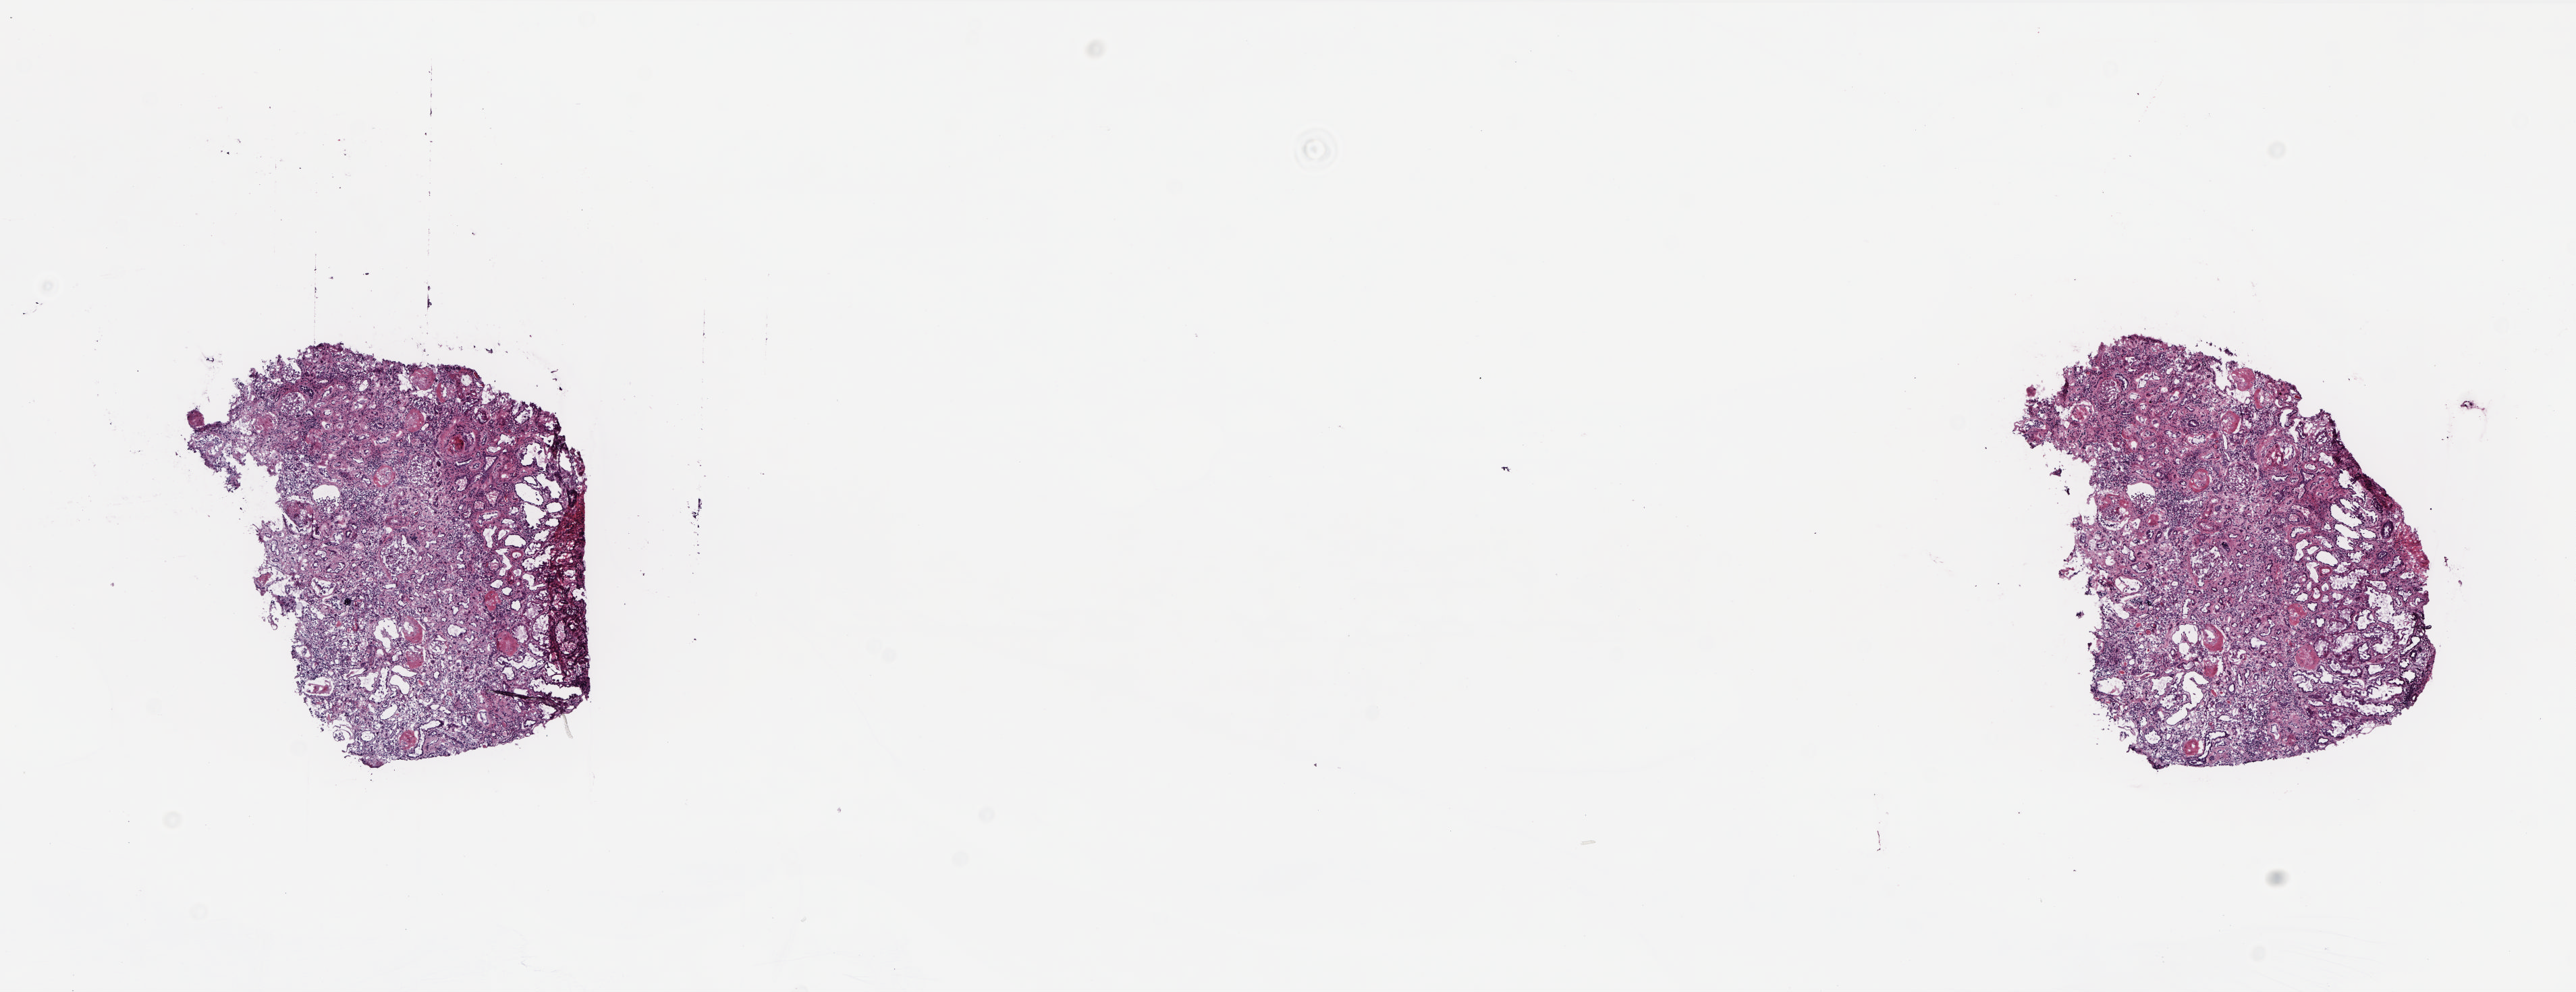
Whole-slide histology image, H&E, a low-resolution overview of the entire scanned area, about 15.4 x 5.9 mm, frozen section from the top of the tissue portion, kidney, solid tissue normal (non-tumour tissue) sample. Male, age 46 years at initial diagnosis. Pathologist review of this section (percent, as recorded): tumour cells 0%, tumour nuclei 0%, normal cells 100%, stromal cells 0%, necrosis 0%. Inflammatory infiltration, as recorded: lymphocyte infiltration 90%, monocyte infiltration 10%, neutrophil infiltration 0%.
* this section: solid tissue normal (non-tumour) sample from the same patient
* patient diagnosis: Papillary adenocarcinoma, NOS